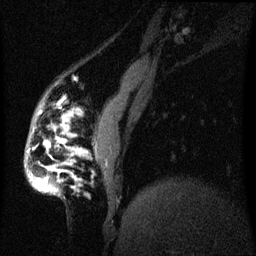
Breast MRI (dynamic contrast-enhanced), one sagittal slice. Slice 10 of 60 in the series (ordered by position). Dynamic contrast-enhanced series, image 2 of 3 at this slice position (ordered by acquisition). 1.5 T. TE 4.2 ms, TR 8 ms. 2.2 mm slice thickness. 256 × 256 image matrix, field of view 200 × 200 mm. Female patient, age 50 years.
Structures marked on this image (semi-automatic segmentation, software-assisted and operator-edited):
- analysis volume of interest (the breast-tissue region the enhancement analysis was run in; not a lesion): bounding box (x1, y1, x2, y2) in pixels: (25, 126, 65, 195)
- tumour enhancement mask (voxels above the 70 % enhancement threshold inside the analysis volume of interest): (38, 146, 49, 189)